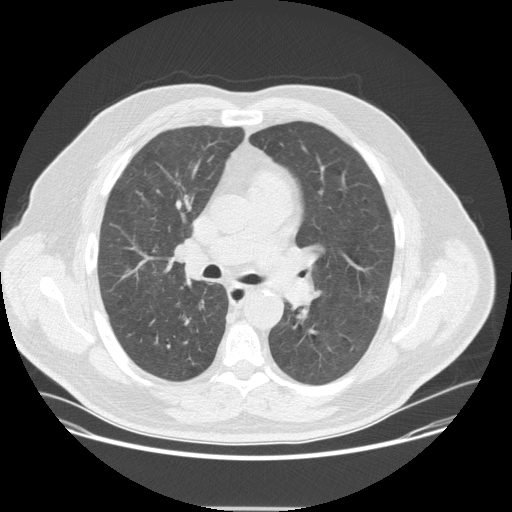
Low-dose screening chest CT, one axial slice. Position 216 of 351 along the scan axis. Reconstruction kernel STANDARD. Lung window (W 1500 / L -600 HU). 512 × 512 image matrix, field of view 419 × 419 mm.
Structures marked on this image (expert manual segmentation):
- lesion 1 (tumor, upper lobe of right lung): bounding box [x1, y1, x2, y2] px = [185, 274, 192, 279]